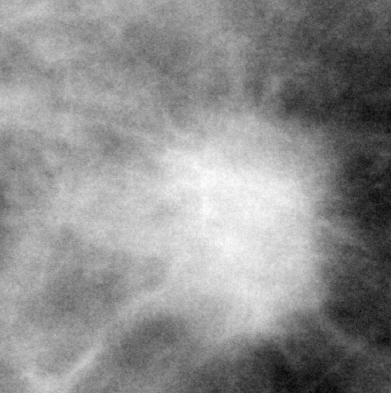
Region of interest cut from a scanned film mammogram (one marked finding); right breast; CC view.
- Finding: mass, shape irregular, margins spiculated; BI-RADS assessment category 5; pathology (as recorded): malignant.